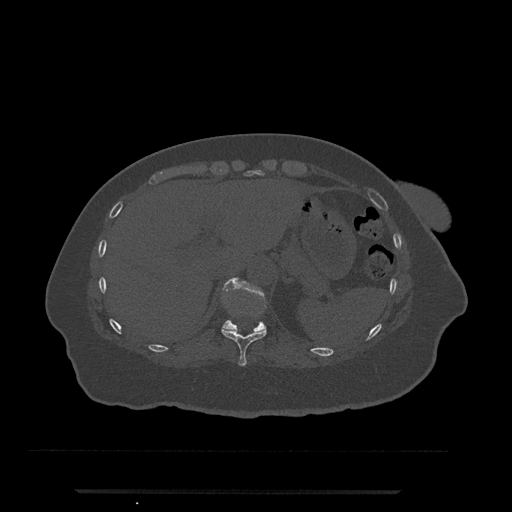
CT including the spine, one axial slice; position 264 of 797 along the scan axis; reconstruction kernel Br40s/3; bone window (W 1800 / L 400 HU); 0.5 mm slice thickness; 512 × 512 image matrix, field of view 440 × 440 mm. Female patient, age 51 years. From the clinical record (not read from this slice): primary cancer: neuro; vertebrae with lytic lesions (as recorded): T8.
Structures marked on this image (semi-automatically segmented with operator editing):
- T10 vertebra: bounding box [x1, y1, x2, y2] px = [221, 327, 267, 366]
- T11 vertebra: [222, 278, 266, 332]